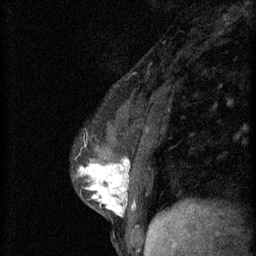
Breast MRI (dynamic contrast-enhanced), one sagittal slice. Slice 20 of 60 in the series (ordered by position). 3 images stored at this slice position (order not interpretable as contrast timing). 1.5 T. TE 4.2 ms, TR 11 ms. 256 × 256 image matrix, field of view 180 × 180 mm. Patient: female, 37 years.
Structures marked on this image (semi-automatically segmented with operator editing):
- analysis volume of interest (the breast-tissue region the enhancement analysis was run in; not a lesion): box from (x=77, y=138) to (x=174, y=221) px
- tumour enhancement mask (voxels above the 70 % enhancement threshold inside the analysis volume of interest): (x=79, y=160)–(x=130, y=217)